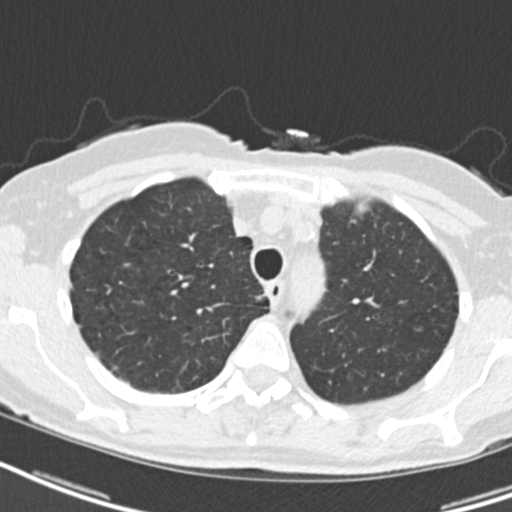
Chest CT (low-dose screening protocol), one axial image, baseline annual screen, lung window (W 1500 / L -600 HU), 2 mm slice thickness, 120 kVp. Female participant, aged 68 years at enrolment. Current smoker at enrolment.
Lesion marked by an expert reader, bounding box (x1, y1, x2, y2) in pixels: (248, 285, 273, 312). No non-calcified nodule or mass ≥4 mm was recorded by the screening reader at this exam. Later outcome: lung cancer diagnosed 807 days after this screen (after the third annual screen) — squamous cell carcinoma, NOS, right upper lobe, mediastinum, poorly differentiated (G3), stage IIIB (AJCC 6th edition), 43 mm at pathology.